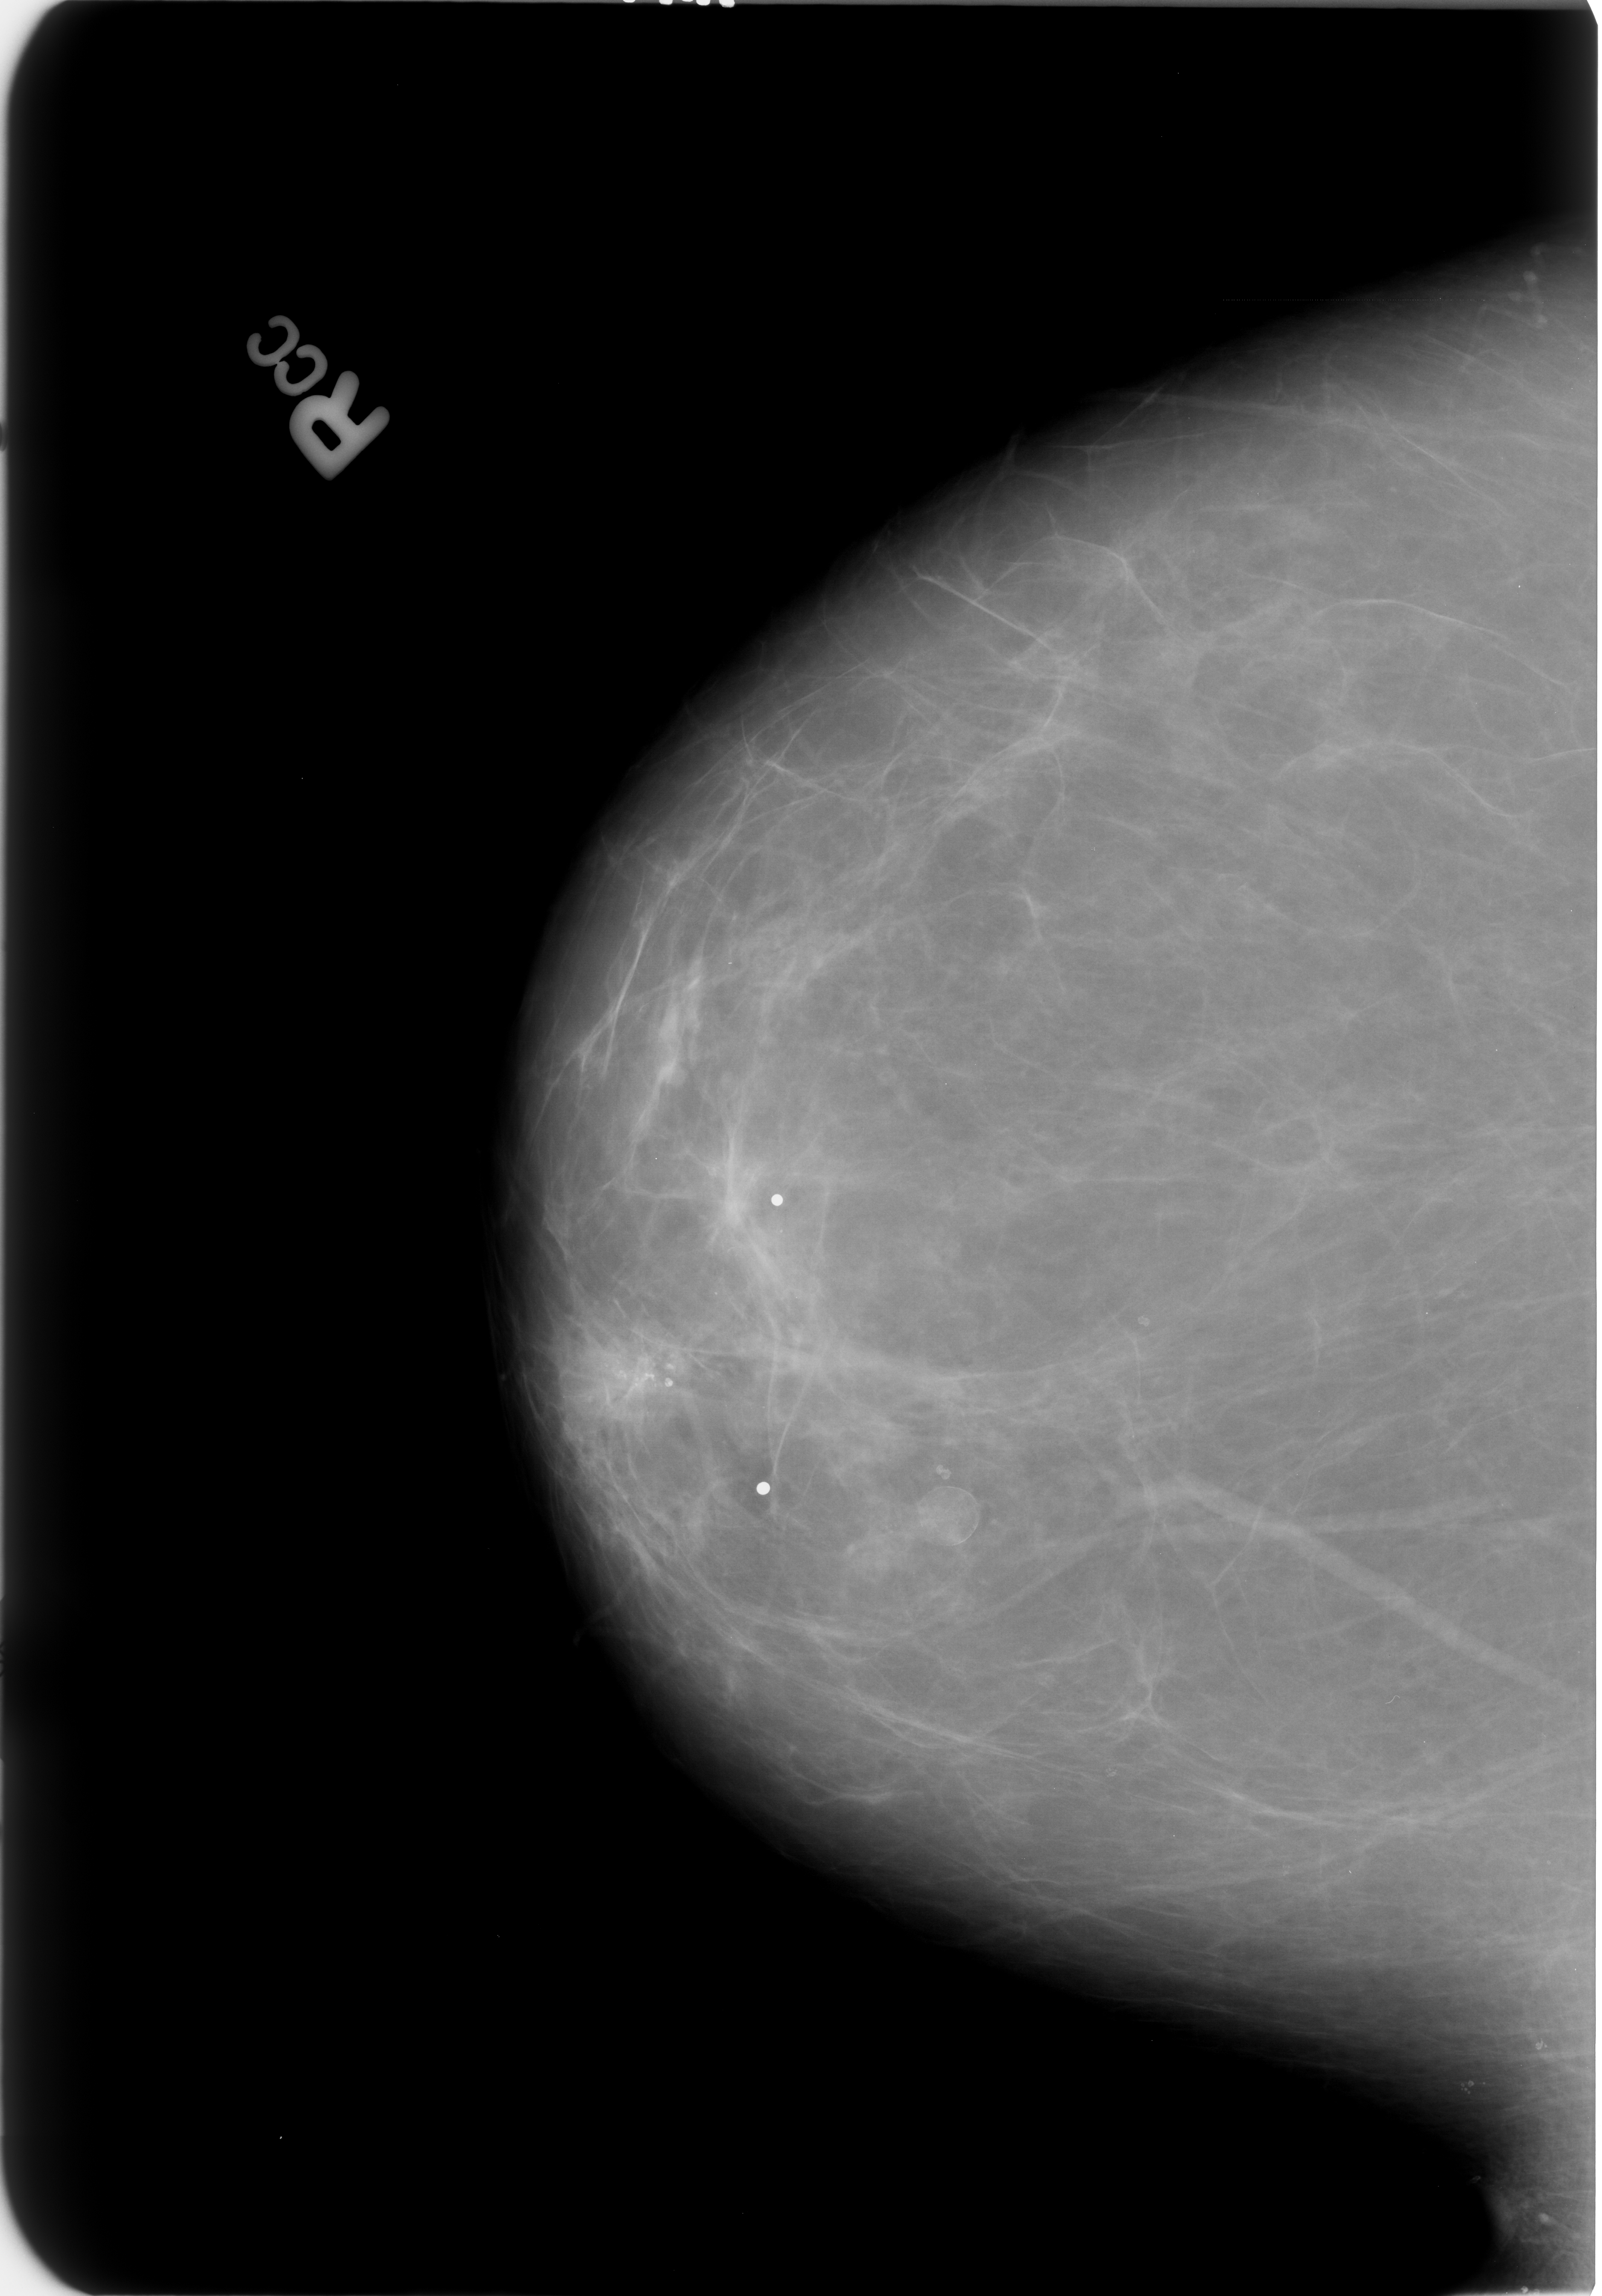
Digitized screen-film mammogram. Right breast. CC view. Breast composition: almost entirely fatty (BI-RADS density category 1 of 4). 1602 × 2296 image matrix.
Marked abnormalities (boxes around the expert regions of interest):
- calcifications, morphology pleomorphic, distribution clustered; BI-RADS assessment category 4; subtlety rating 4 on a 1 (subtle) to 5 (obvious) scale; pathology result (as recorded, not read from the image): benign: bounding box [x1, y1, x2, y2] px = [537, 1301, 698, 1424]